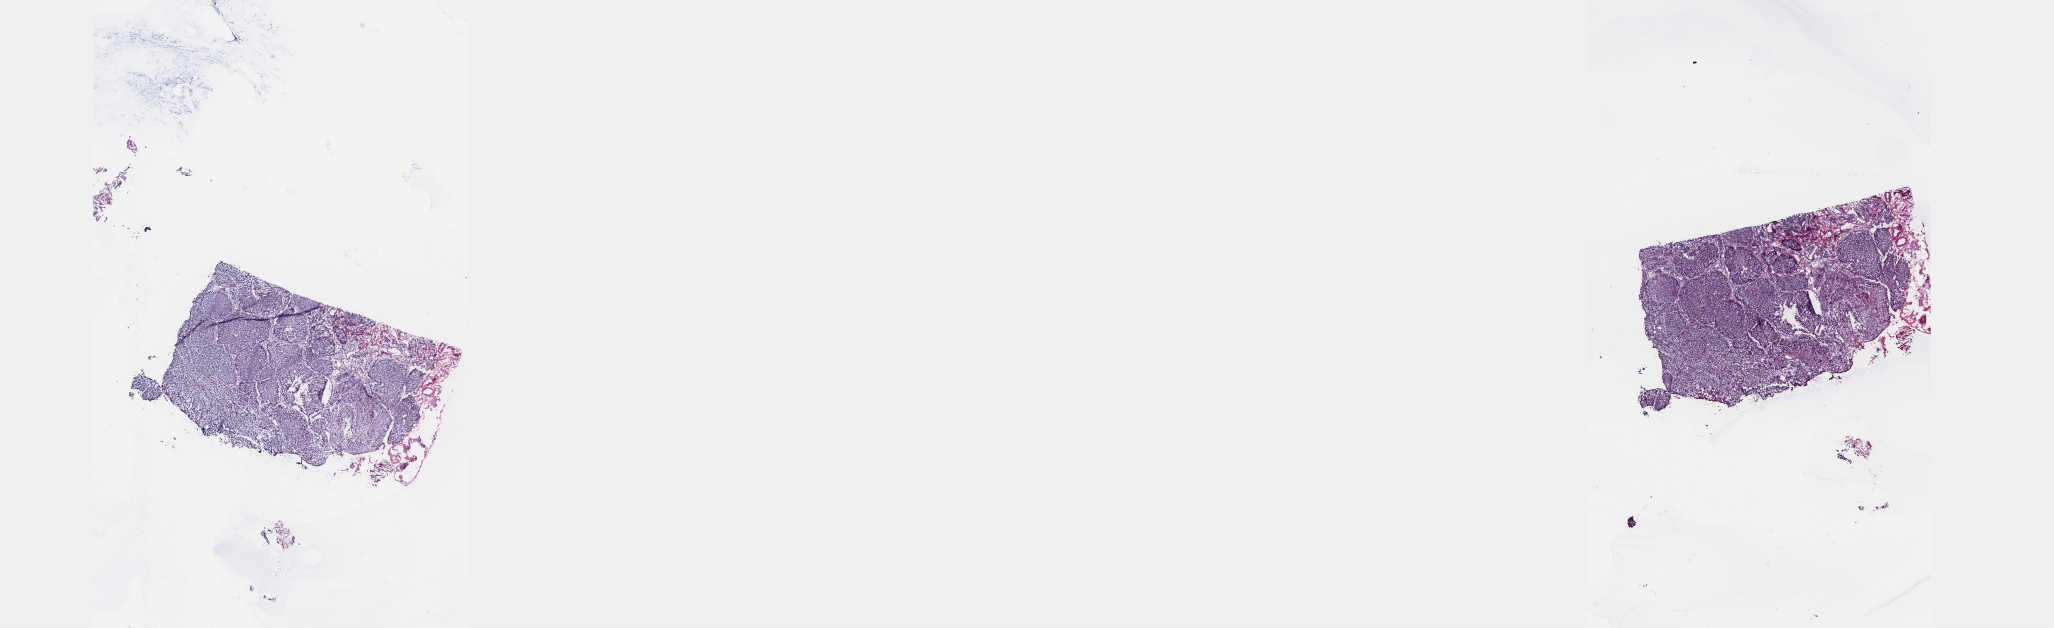
H&E-stained whole-slide image, whole scanned area (about 33.2 x 10.1 mm) shown as a low-resolution overview; frozen section from the top of the tissue portion; esophagus, primary tumour sample. Male patient; age at initial diagnosis 54 years. Slide review estimates, as recorded: tumour cells 80%, tumour nuclei 80%.
Diagnosis: Squamous cell carcinoma, NOS (lower third of esophagus).